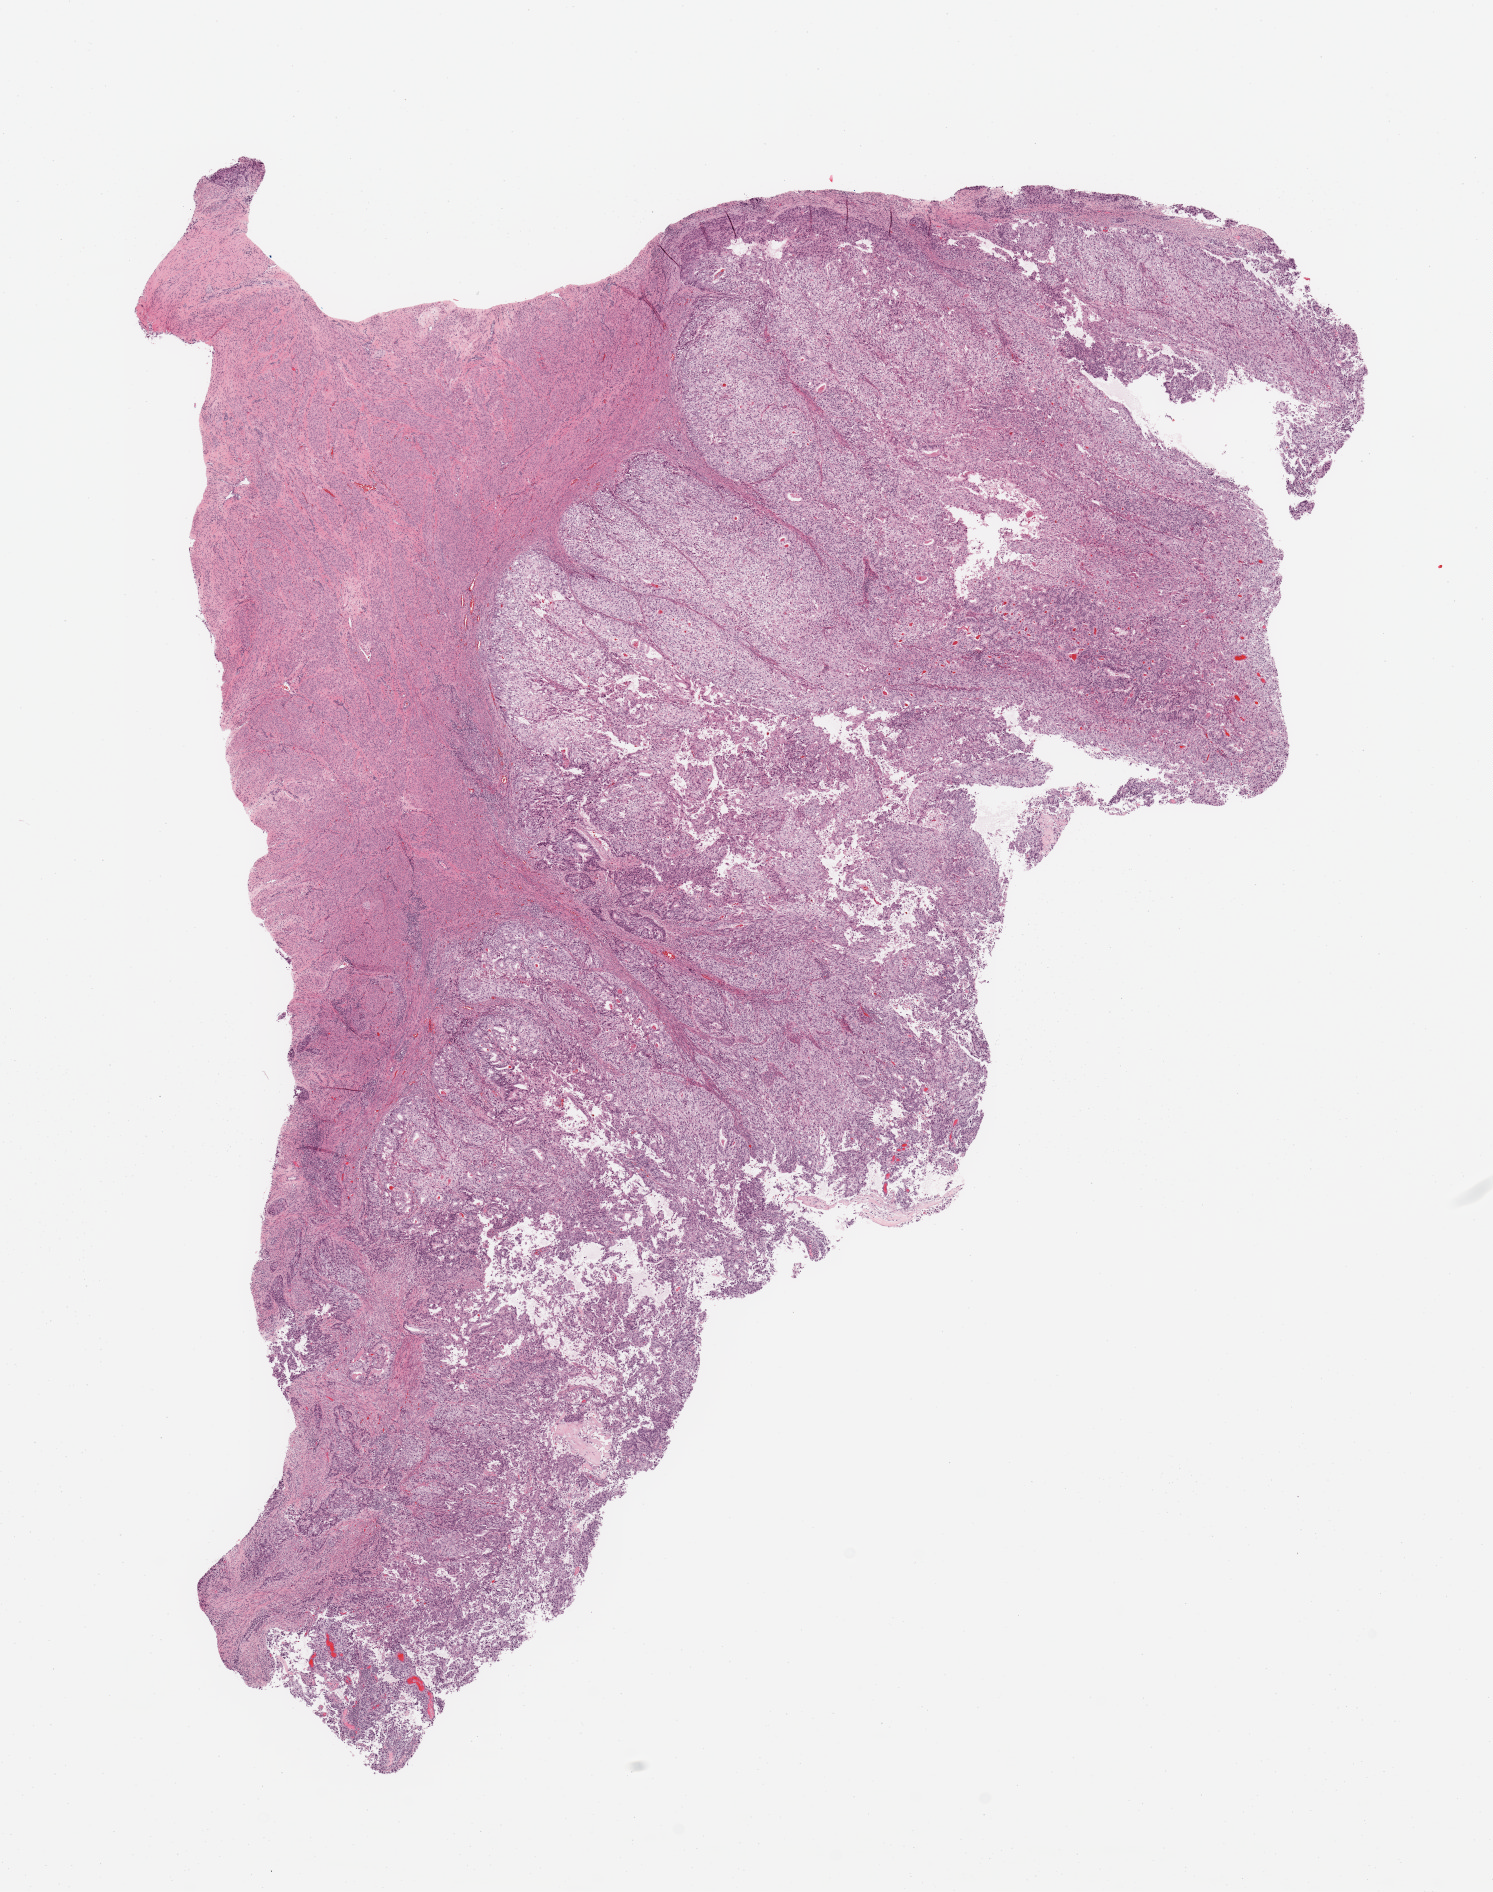
H&E-stained whole-slide image — a low-resolution overview of the entire scanned area, about 11.8 x 15.0 mm (acquisition: 20x scan); tumour tissue sample, sampled site: uterus. 67-year-old female patient. Histologic grade: G3 (poorly differentiated). Slide review estimates, as recorded: tumour nuclei 80%, necrosis 0%.
- AJCC pathologic stage: IVB
- histologic diagnosis: Endometrioid adenocarcinoma, NOS
- primary tumour site (as recorded): anterior endometrium